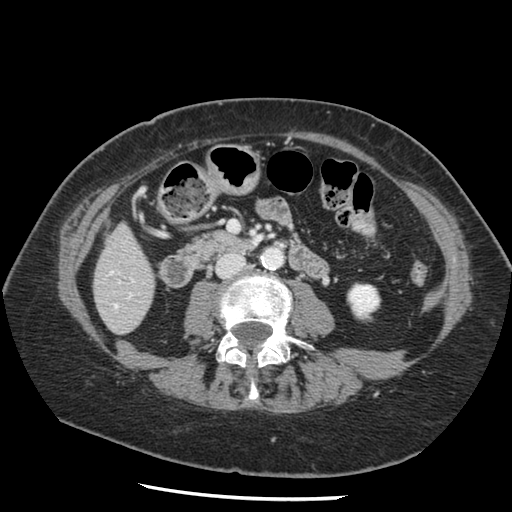
Contrast-enhanced abdominal CT, one axial slice; position 32 of 148 along the scan axis; reconstruction kernel STANDARD; intravenous contrast given; soft-tissue window (W 400 / L 40 HU); 2.5 mm slice thickness; 512 × 512 image matrix, field of view 330 × 330 mm. Female patient, age 85 years. From the clinical record (not read from this slice): diagnosis: colorectal cancer liver metastases, imaged before liver resection; multiple liver metastases: no; largest metastasis: 0.9 cm; disease in both lobes: no.
Outlined on this slice (expert manual segmentation):
- hepatic veins: bounding box <110,272,116,306> (left, top, right, bottom; pixels)
- liver: <95,226,154,334>
- planned liver remnant (the part of the liver to remain after resection): <95,226,154,332>